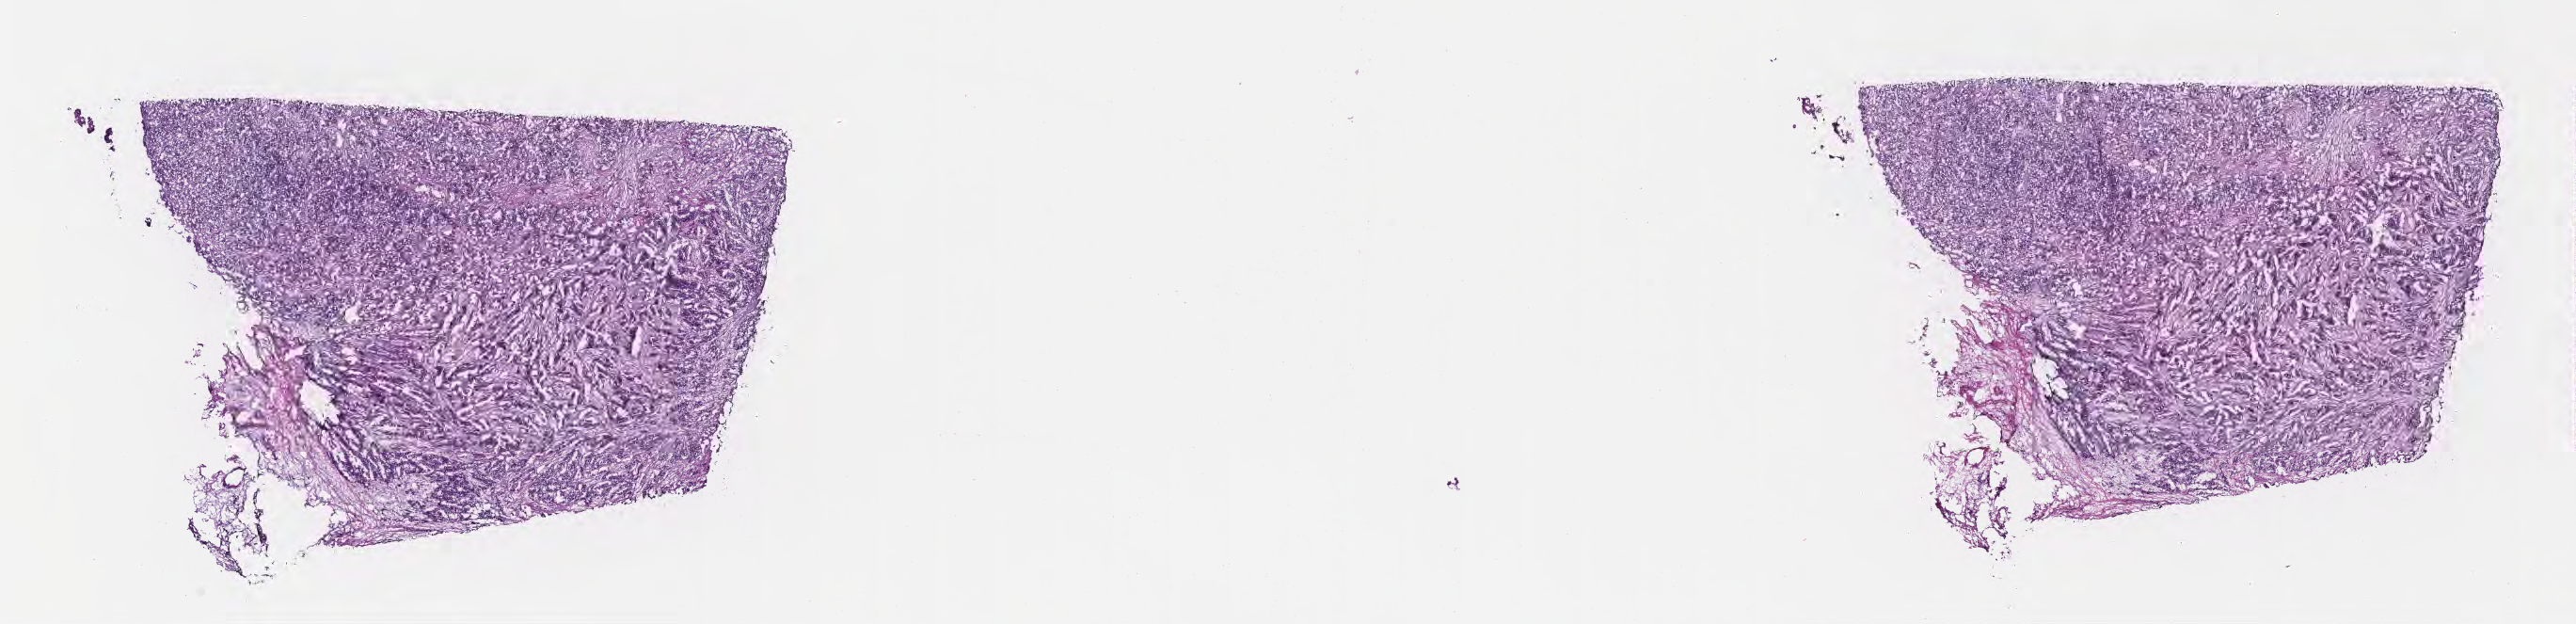
Digitized hematoxylin and eosin (H&E)-stained section, low-resolution overview of the scanned area, about 22.1 x 5.4 mm; frozen section; metastatic tumor tissue, resected from lymph node. Patient: male, age at initial diagnosis 71 years. Composition of this section per pathologist review: tumor cells 85%, tumor nuclei 85%, stromal cells 15%, necrosis 0%, normal cells 0%. Infiltration values recorded for this section: lymphocyte infiltration 4%, monocyte infiltration 2%, neutrophil infiltration 3%.
Section: bottom of the tissue portion. Patient diagnosis (primary): Neuroendocrine carcinoma, NOS.